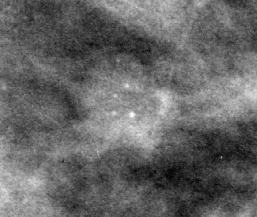
Crop from a digitized film mammogram around one marked abnormality; left breast; CC view.
Finding: calcifications, morphology punctate, distribution clustered; BI-RADS assessment category 4; subtlety rating 3 on a 1 (subtle) to 5 (obvious) scale; pathology (as recorded): benign.